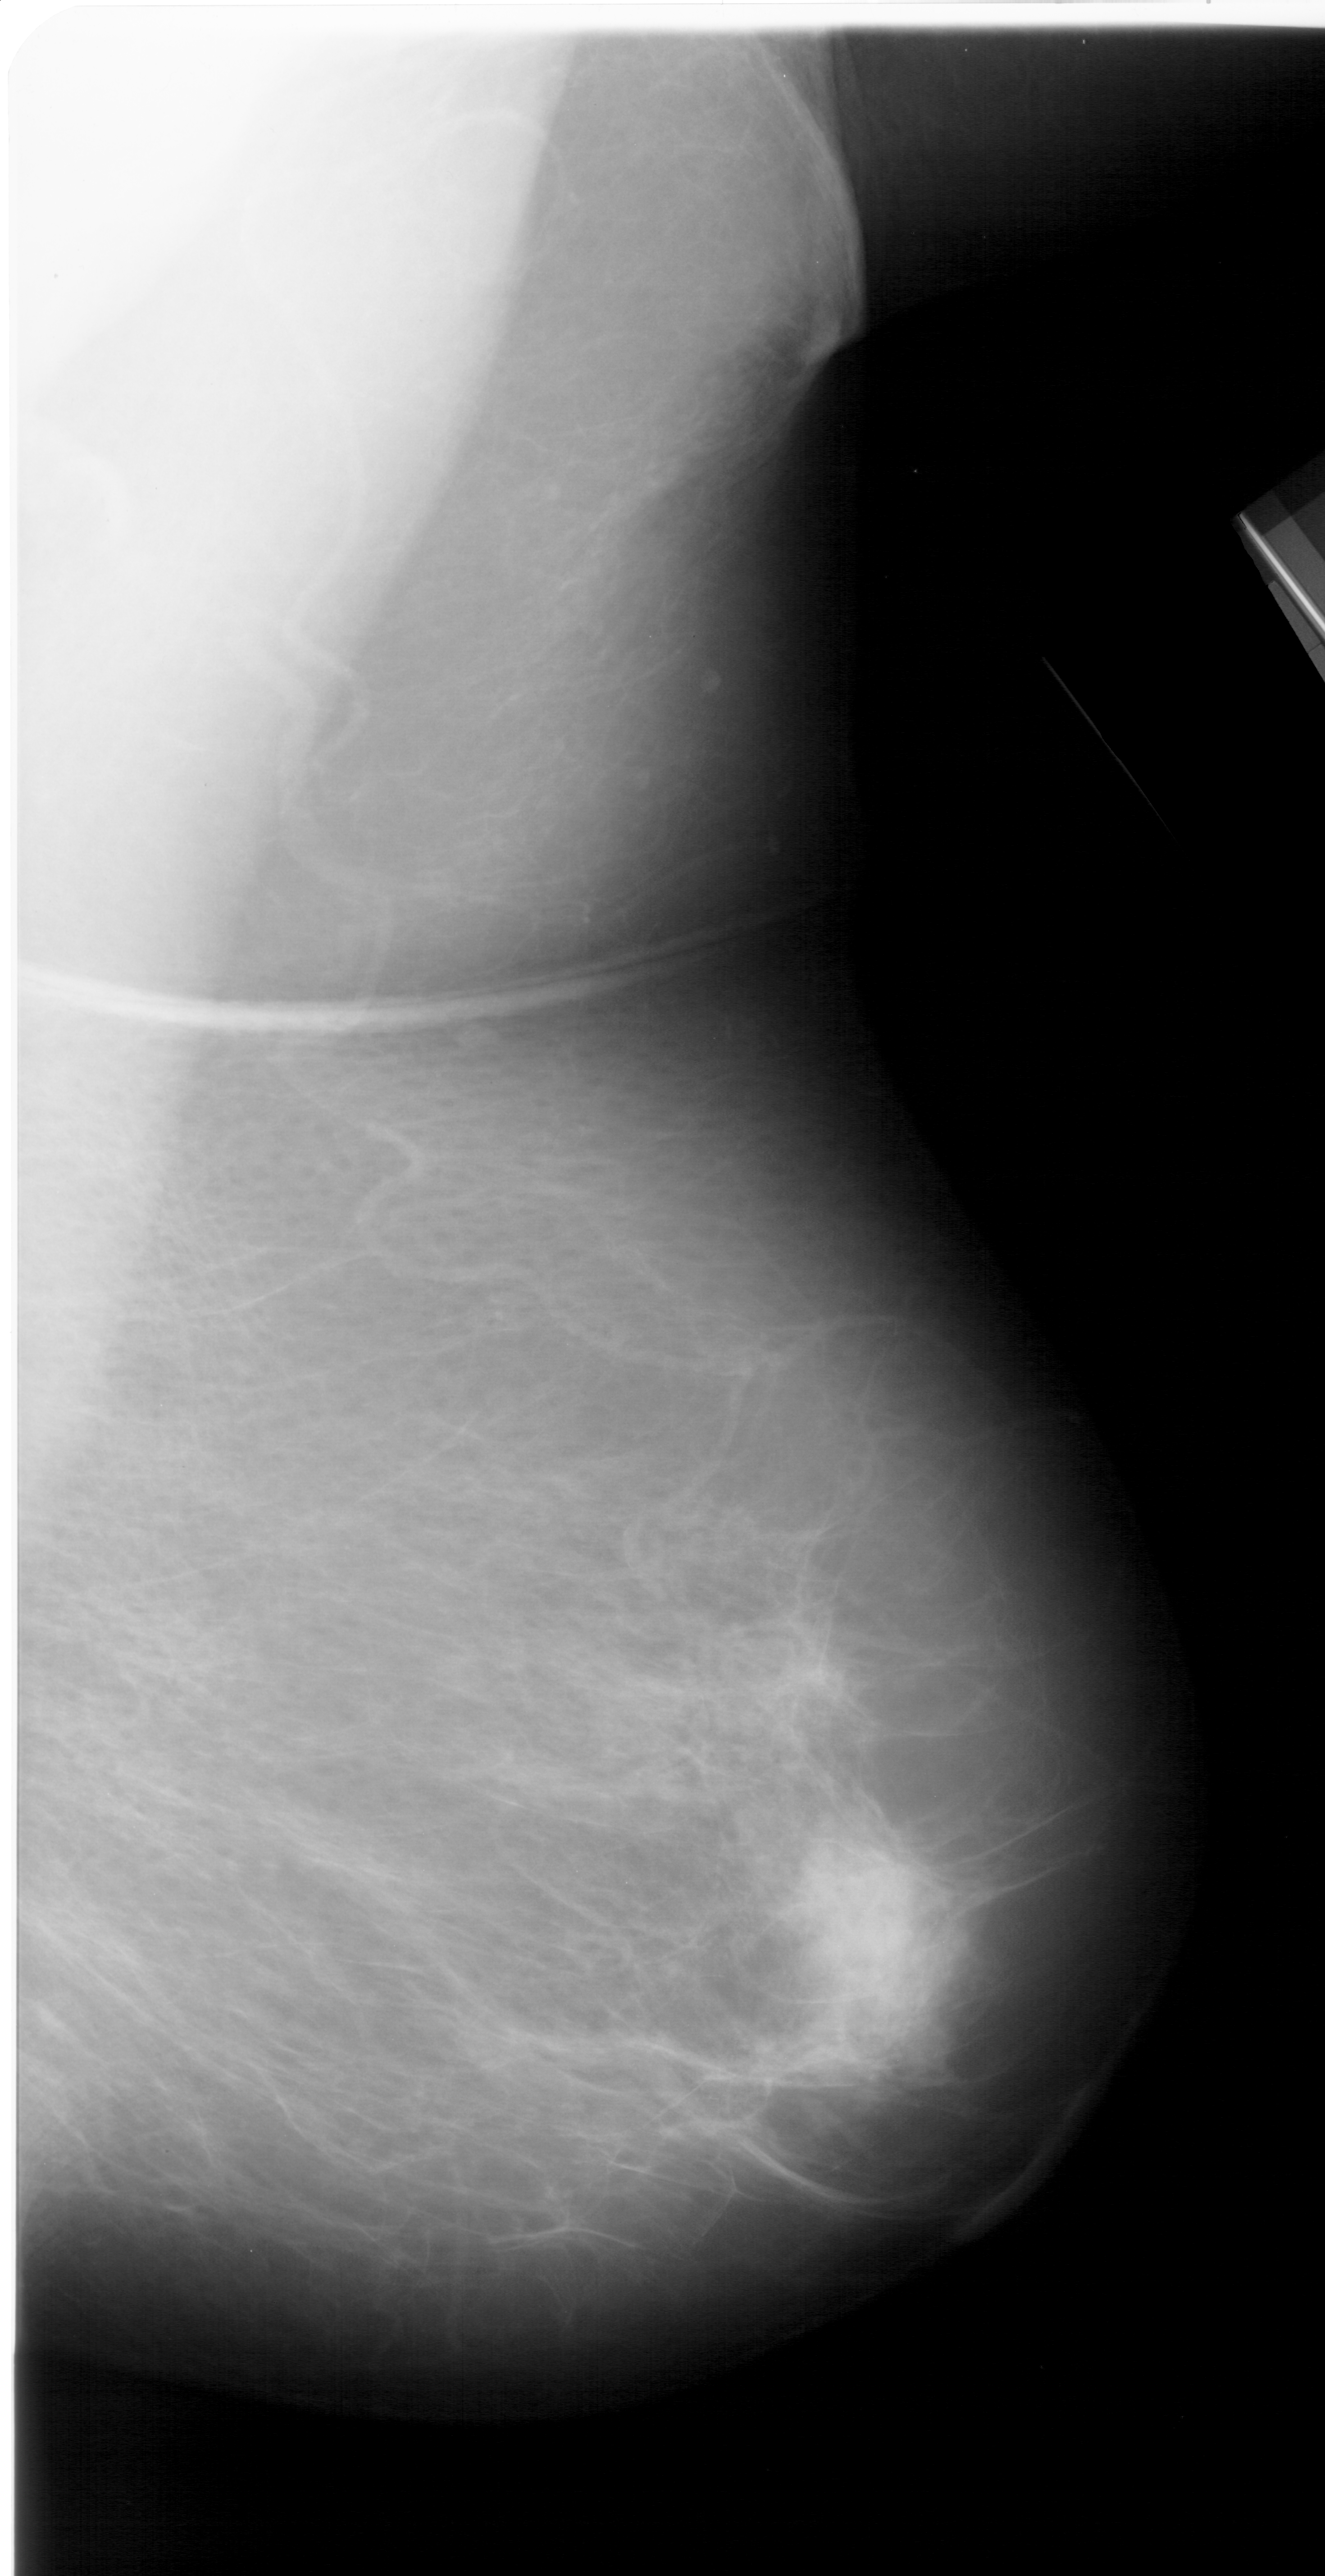
Scanned film-screen mammogram; right breast; mediolateral oblique (MLO) view; BI-RADS breast density category 3 (scale 1–4); 1325 × 2576 image matrix.
Marked abnormalities (boxes around the expert regions of interest):
- mass, shape irregular, margins ill defined; BI-RADS assessment category 4; subtlety rating 4 on a 1 (subtle) to 5 (obvious) scale; pathology (as recorded): benign: bounding box <783,1843,972,2062> (left, top, right, bottom; pixels)